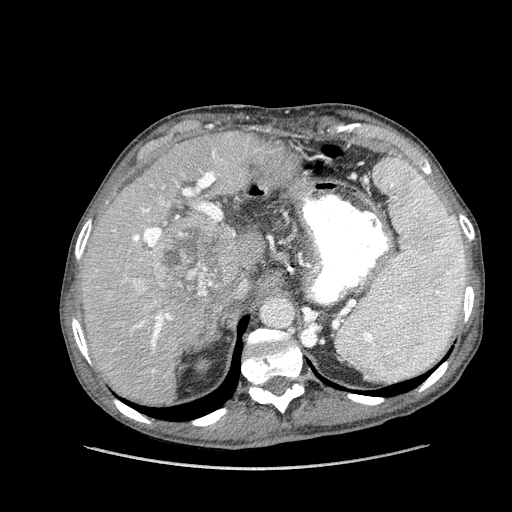
Contrast-enhanced abdominal CT (liver protocol), one axial slice; slice 99 of 162 in the series (ordered by position); reconstruction kernel STANDARD; soft-tissue window (W 400 / L 40 HU); 2.5 mm slice thickness; 512 × 512 image matrix, field of view 400 × 400 mm. From the clinical record (not read from this slice): diagnosis: hepatocellular carcinoma (patient treated with transarterial chemoembolisation; whether this scan precedes or follows treatment is not stated here); TNM stage (as recorded): Stage-IIIA; Child-Pugh class: A.
Structures marked on this image (semi-automatic segmentation, software-assisted and operator-edited):
- liver parenchyma outside the tumour (the mass and vessels are separate outlines, so this box may not span the whole liver): bounding box [x1, y1, x2, y2] px = [82, 132, 296, 404]
- mass: [151, 212, 242, 306]
- liver vessels: [96, 150, 235, 373]